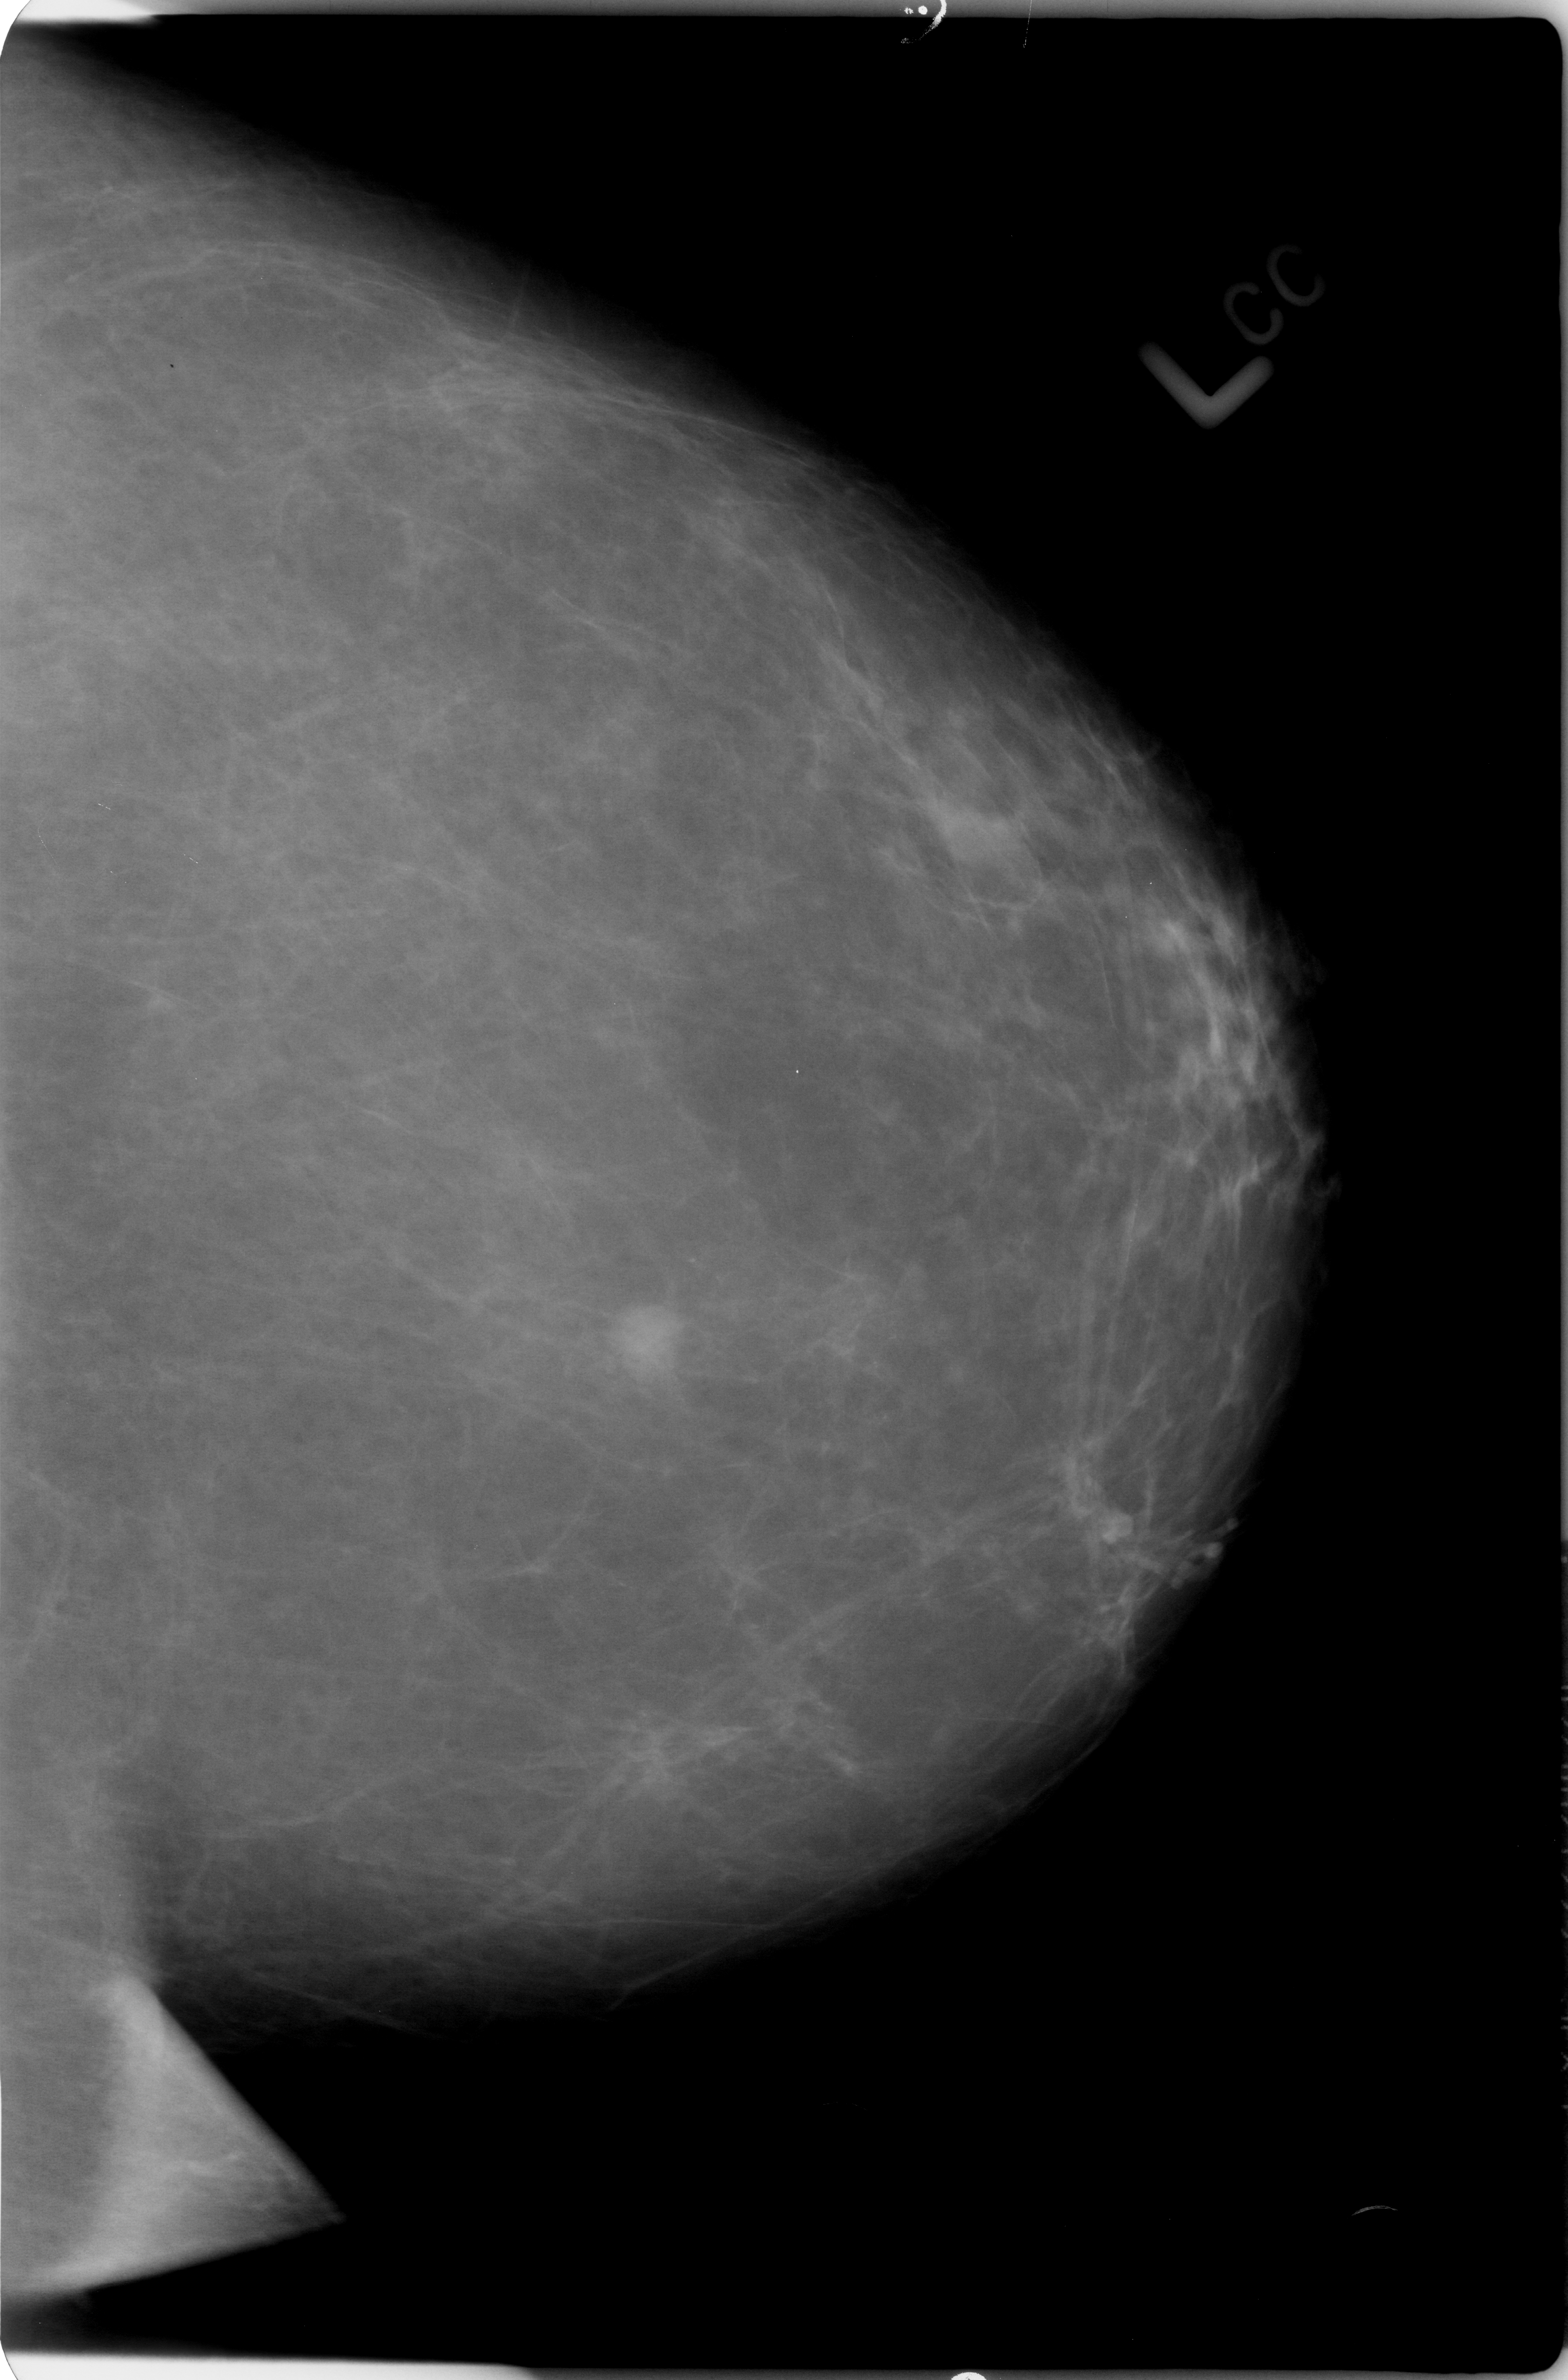
Scanned film-screen mammogram. Left breast. Craniocaudal (CC) view. Breast composition: almost entirely fatty (BI-RADS density category 1 of 4). 1568 × 2380 image matrix.
Expert-marked regions of interest on this film, with their recorded descriptors:
- mass, shape lobulated, margins ill defined; BI-RADS assessment category 4; subtlety rating 4 on a 1 (subtle) to 5 (obvious) scale; pathology (as recorded): malignant: box from (x=610, y=1303) to (x=685, y=1380) px